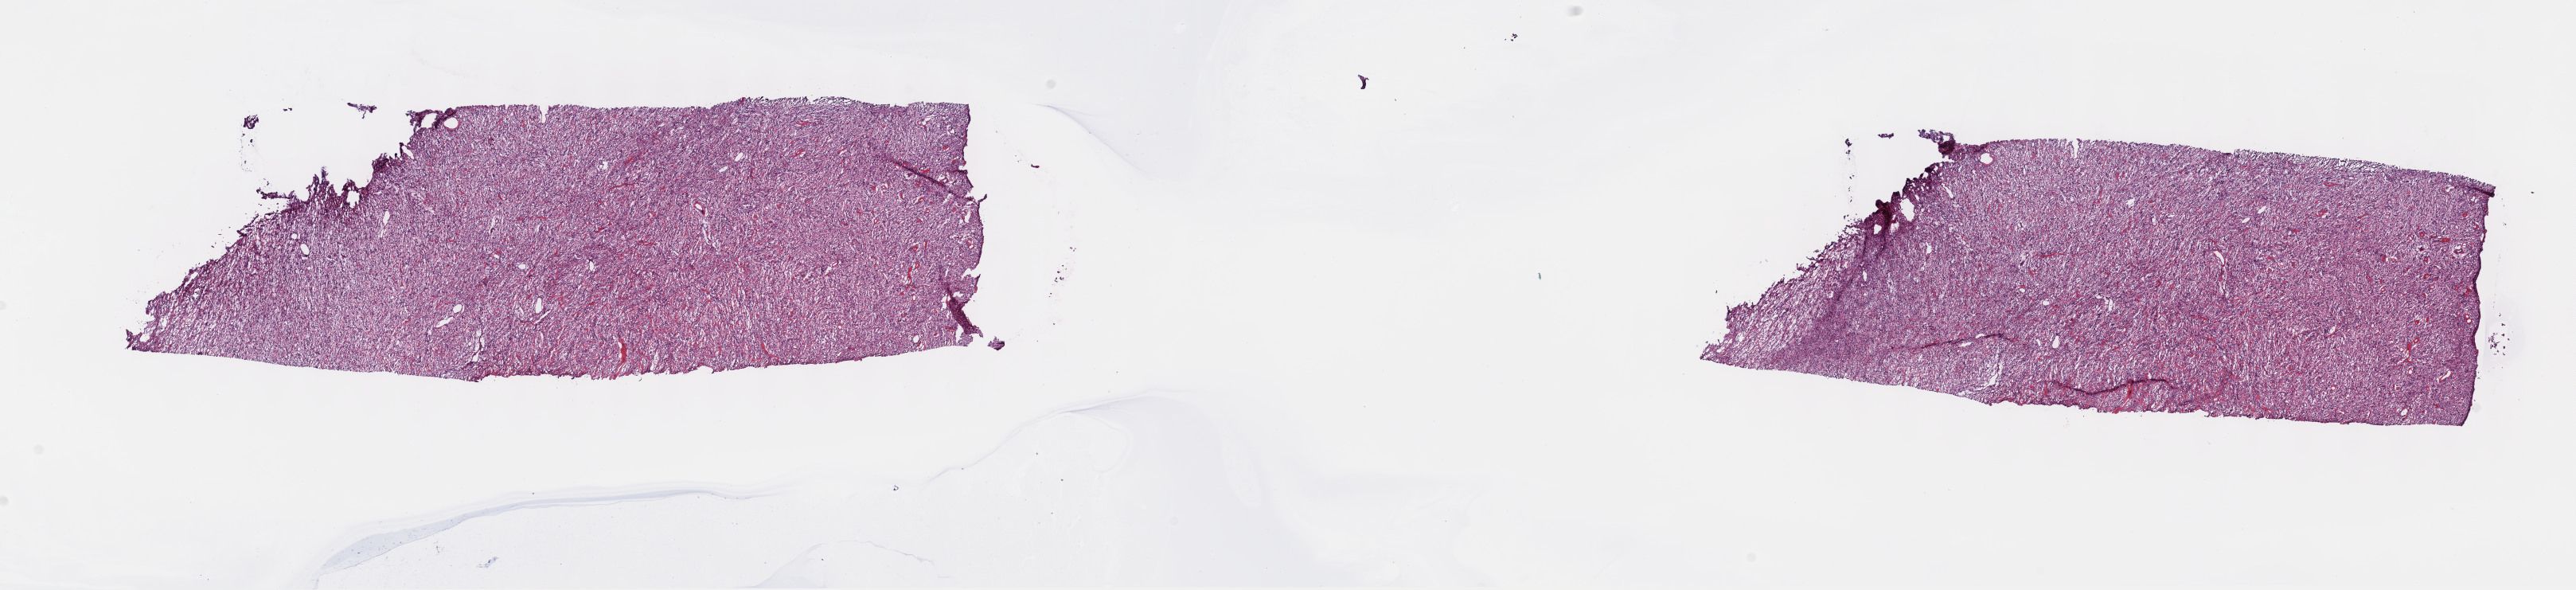
H&E whole-slide image, low-resolution overview of the scanned area, about 26.2 x 6.0 mm (slide scanned at 40x); frozen section from the top of the tissue portion; metastatic tumour sample, sampled site not recorded. Male patient; age at initial diagnosis 26 years. Composition of this section per pathologist review: tumour cells 90%, tumour nuclei 95%, normal cells 0%, stromal cells 10%, necrosis 0%. Inflammatory infiltration, as recorded: lymphocyte infiltration 0%, monocyte infiltration 0%, neutrophil infiltration 0%.
* this section: metastatic tumour tissue
* patient diagnosis: Spindle cell melanoma, NOS